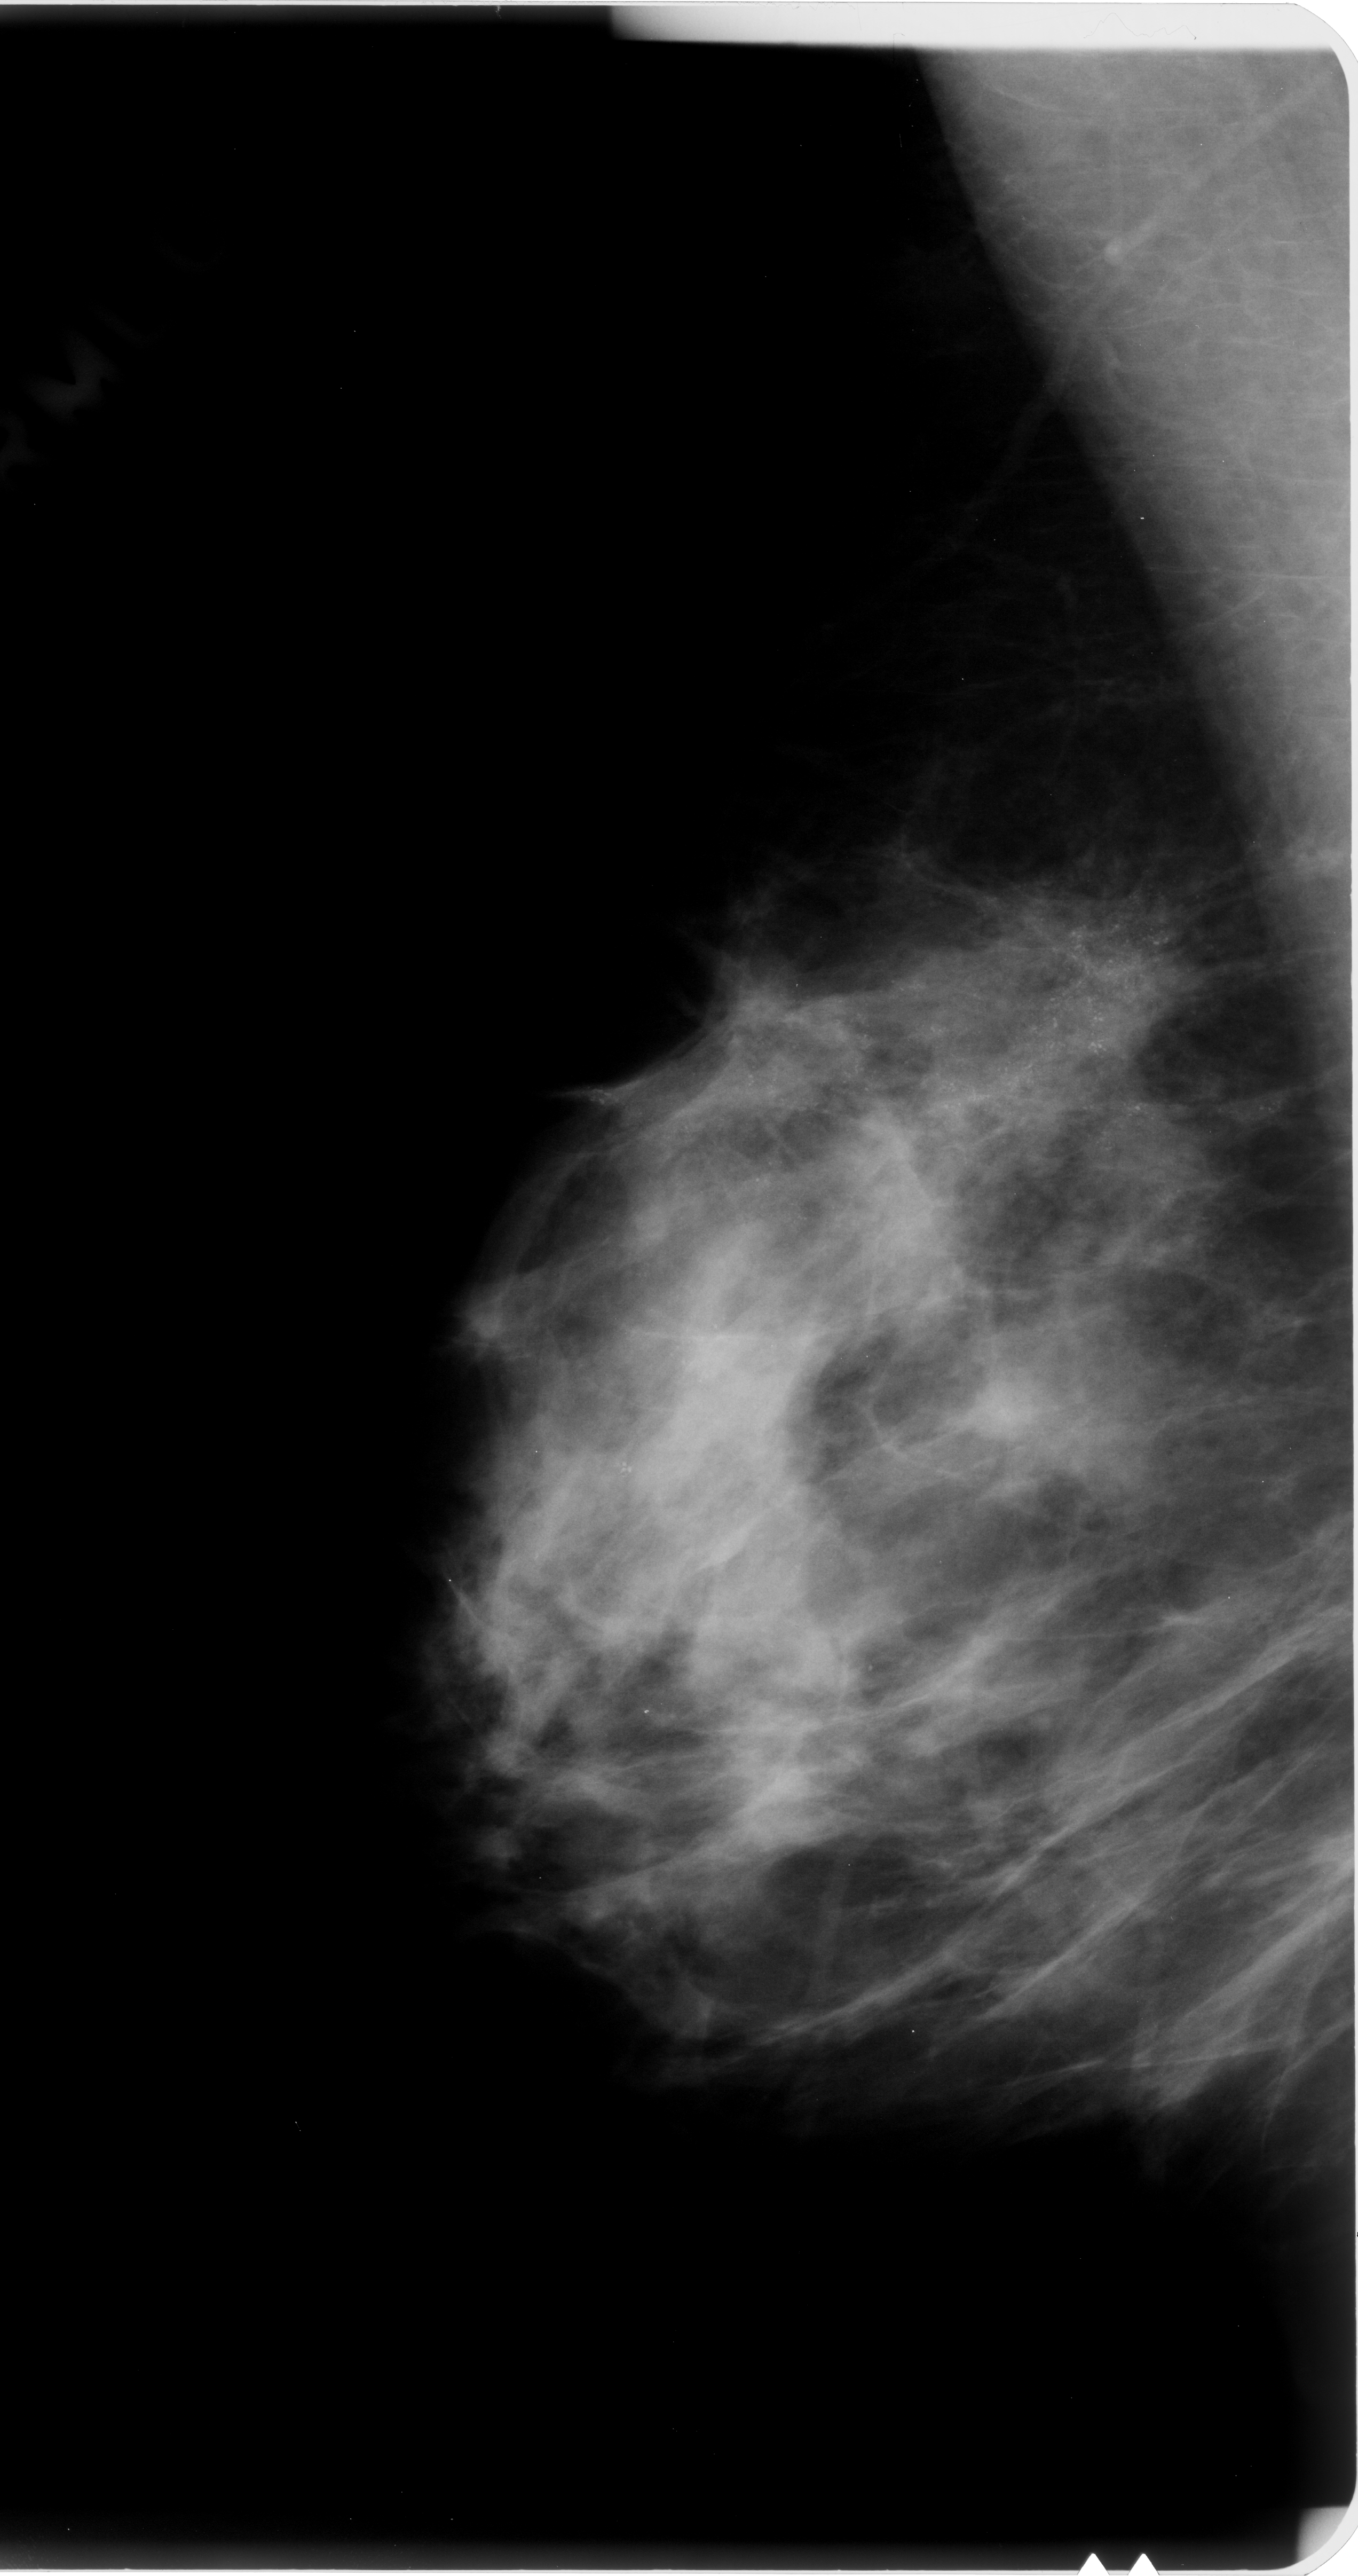
Digitized screen-film mammogram; right breast; mediolateral oblique (MLO) view; breast composition: heterogeneously dense (BI-RADS density category 3 of 4); 1358 × 2576 image matrix.
Marked abnormalities (boxes around the expert regions of interest):
- calcifications, morphology pleomorphic, distribution regional; BI-RADS assessment category 5; subtlety rating 5 on a 1 (subtle) to 5 (obvious) scale; pathology result (as recorded, not read from the image): malignant: bounding box (x1, y1, x2, y2) in pixels: (414, 760, 1316, 1599)